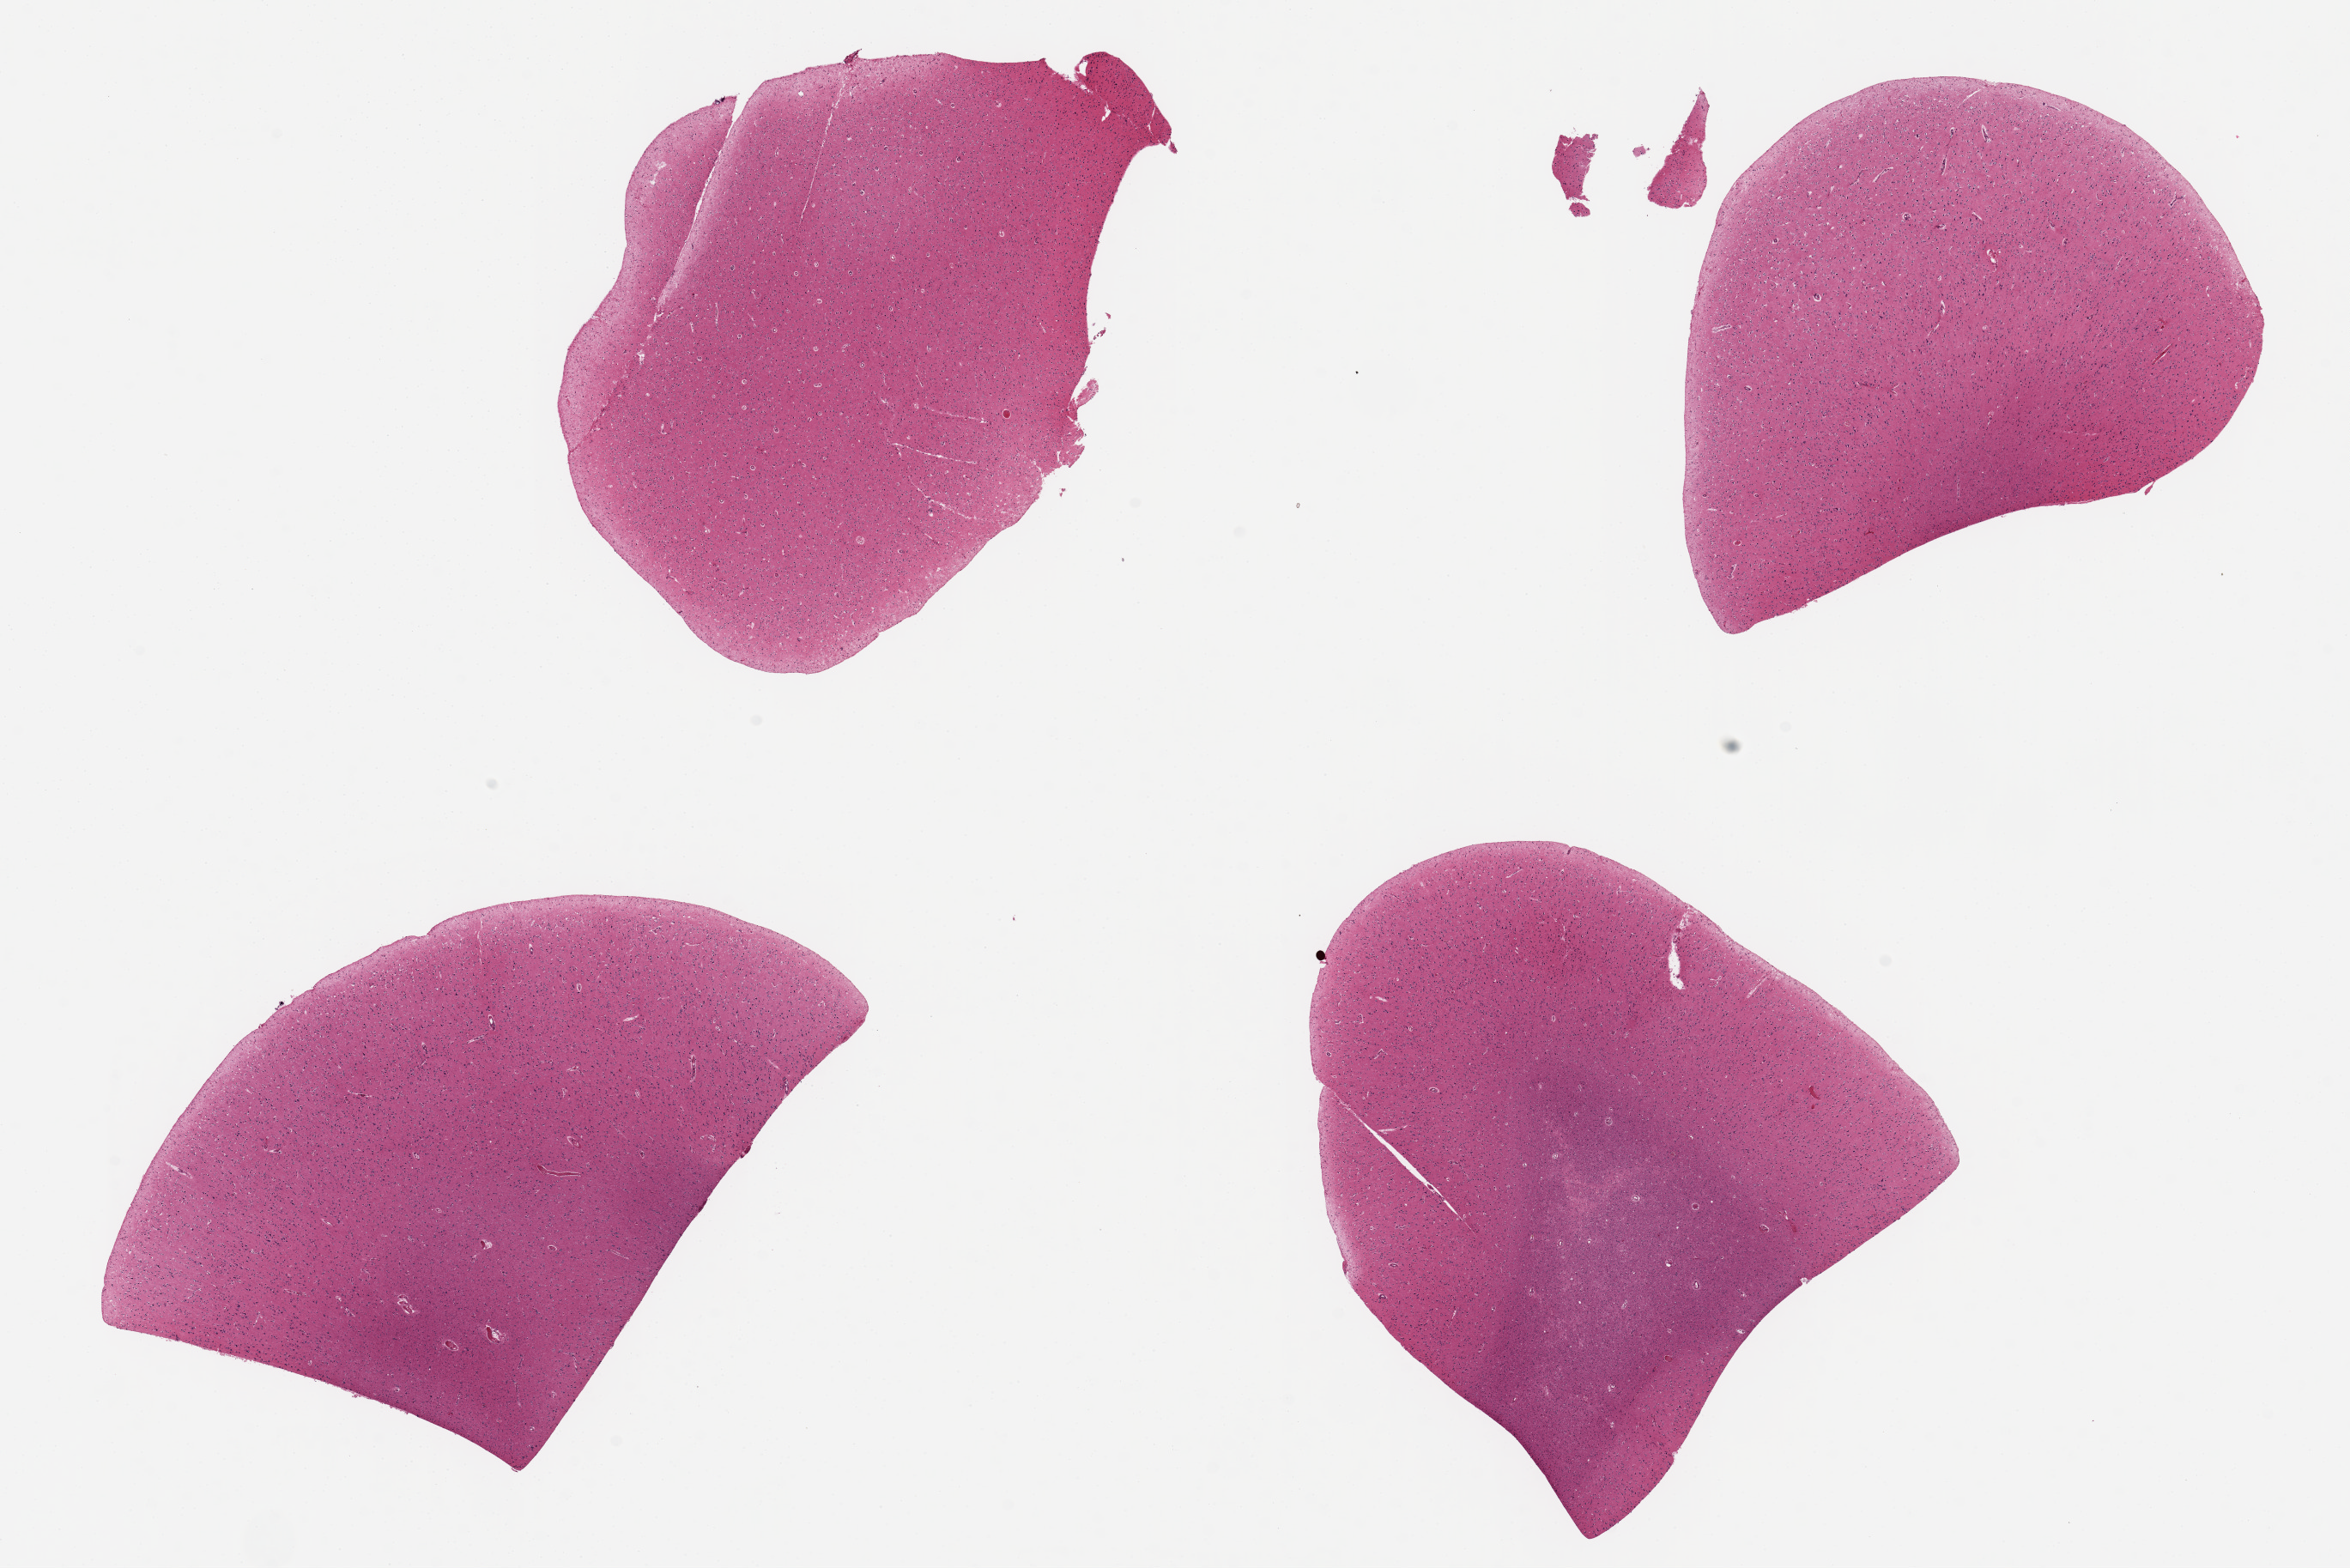
Digitized H&E-stained section — a low-resolution overview of the entire scanned area, about 21.7 x 14.5 mm (acquisition: 20x scan); PAXgene-fixed paraffin-embedded (PFPE) section; section of cerebral cortex (target tissue); tissue donor sample. Donor: male.
Review note (as recorded): 4 ~6x4mm aliquots.